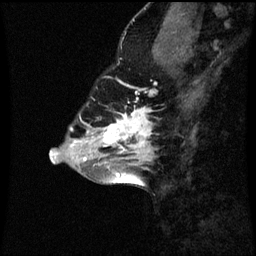
Breast MRI (dynamic contrast-enhanced), one sagittal slice. Slice 24 of 60 in the series (ordered by position). Dynamic contrast-enhanced series, image 2 of 3 at this slice position (ordered by acquisition). 1.5 T. TE 4.2 ms, TR 8.9 ms. 2 mm slice thickness. 256 × 256 image matrix, field of view 200 × 200 mm. Patient: female, 43 years. Case-level facts recorded for this patient, not image findings: setting: breast cancer imaged before/during neoadjuvant chemotherapy; receptor status: HR-positive, HER2-negative.
Outlined on this slice (semi-automatic segmentation, software-assisted and operator-edited):
- analysis volume of interest (the breast-tissue region the enhancement analysis was run in; not a lesion): bounding box (x1, y1, x2, y2) in pixels: (96, 106, 159, 159)
- tumour enhancement mask (voxels above the 70 % enhancement threshold inside the analysis volume of interest): (104, 108, 153, 153)